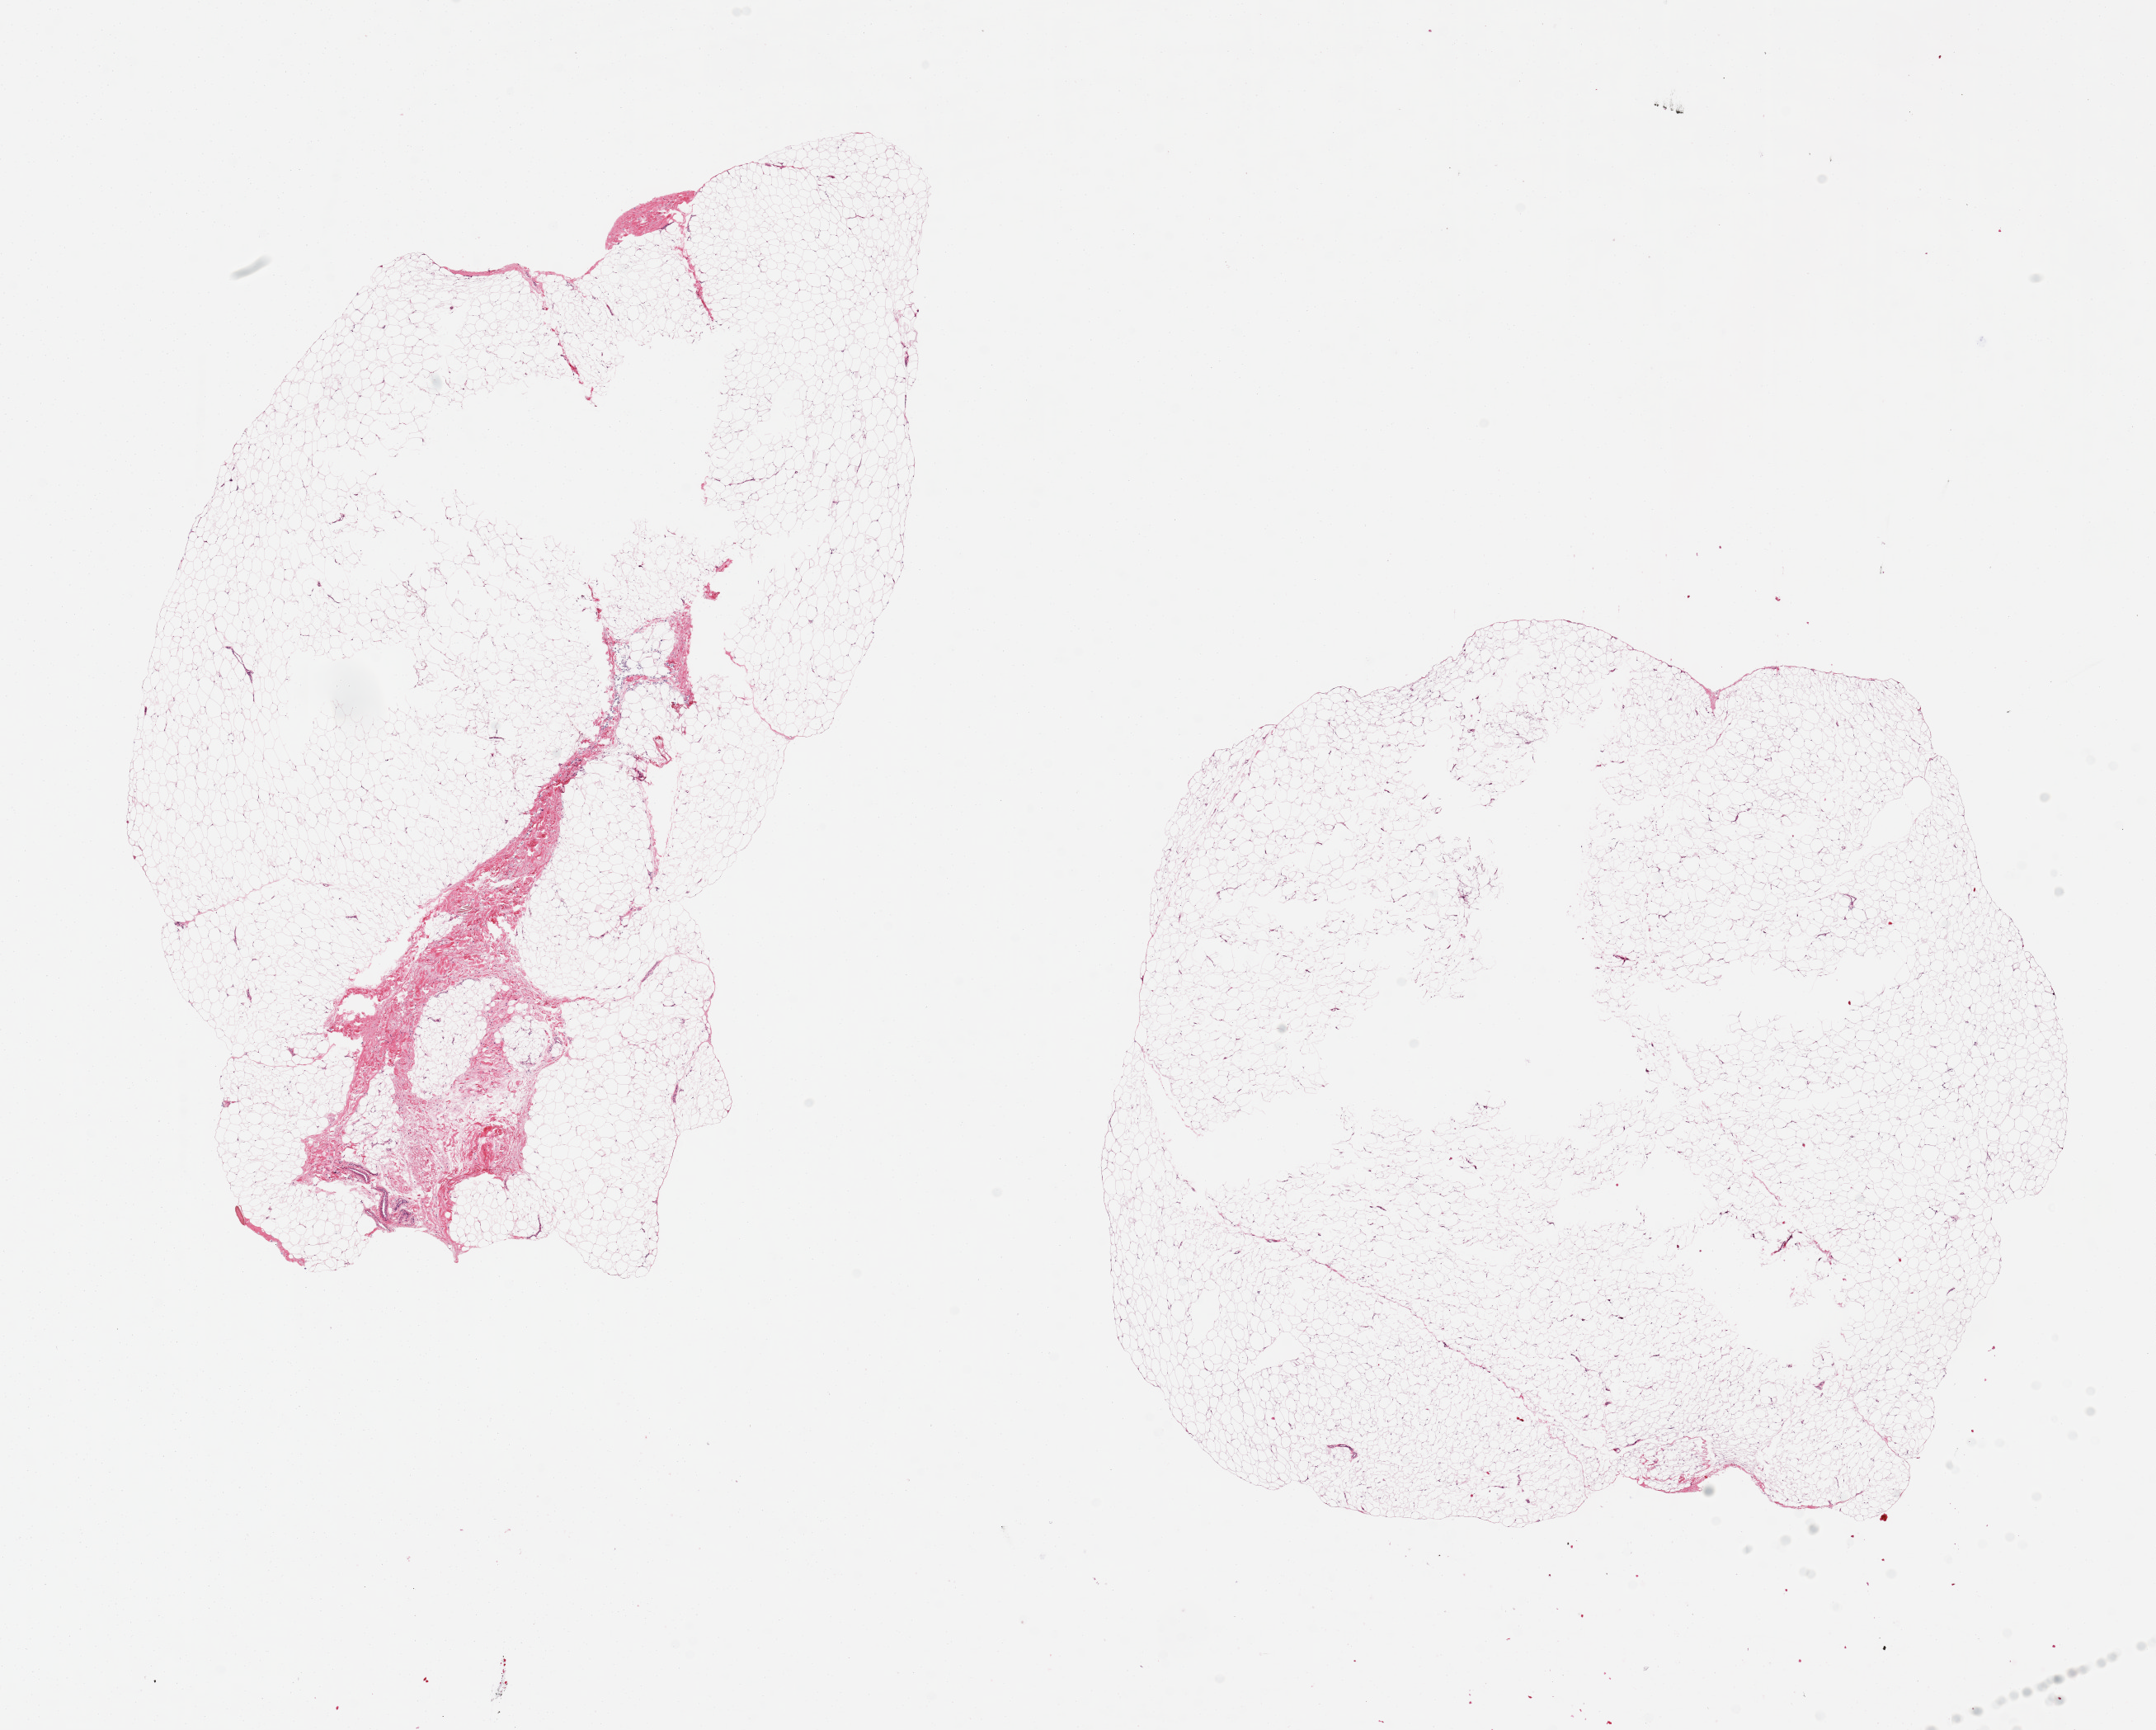
Digitized H&E-stained section — a low-resolution overview of the entire scanned area, about 20.7 x 16.6 mm; PAXgene-fixed paraffin-embedded (PFPE) section; sampled site (target tissue): adipose tissue; tissue donor sample. Donor sex: male.
Pathologist's review note for this sample: 2 pieces ~12x7 & 9x9 mm; up to 10% centrally empty (unfixed or fractured).